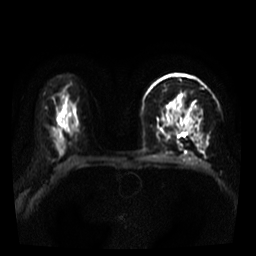
Breast MRI, one axial slice; position 25 of 39 along the scan axis; diffusion-weighted series; image 2 of 4 stored at this slice position (different b-values; order by instance number); 3 T; 5 mm slice thickness; 256 × 256 image matrix, field of view 320 × 320 mm. Female patient.
Annotated regions visible in this slice (expert manual segmentation):
- tumour on diffusion-weighted imaging: bounding box <195,108,200,120> (left, top, right, bottom; pixels)